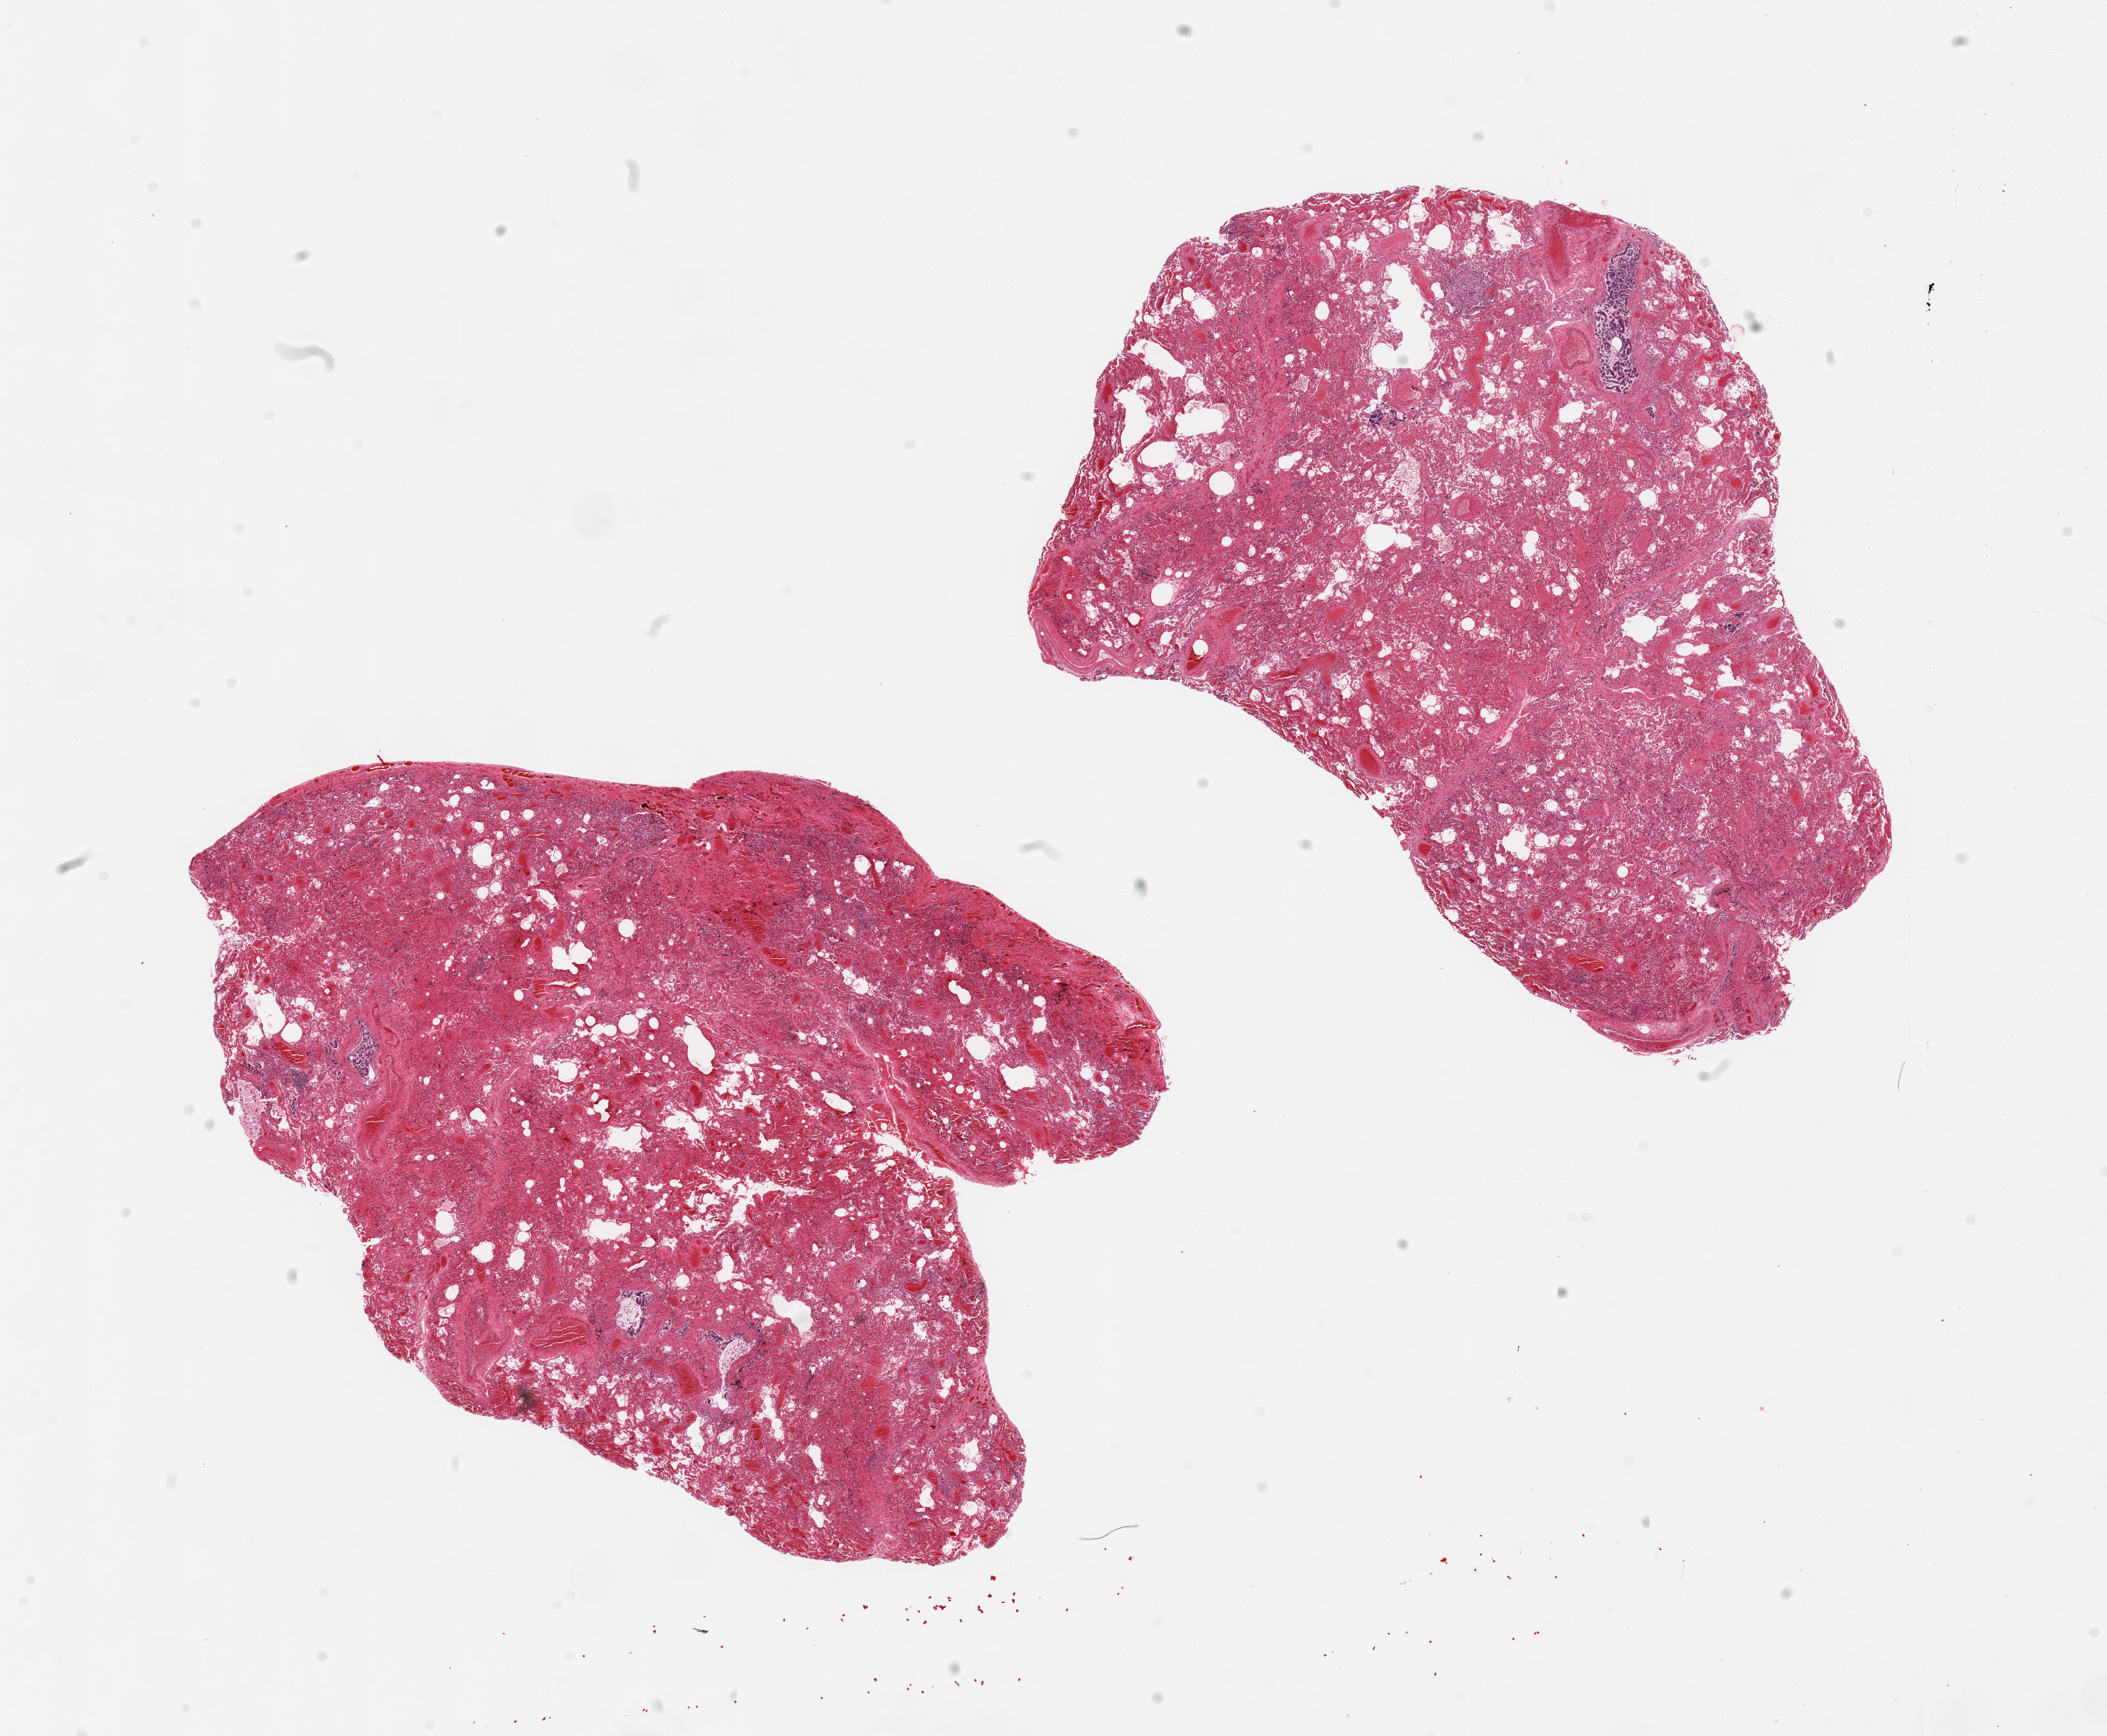
Whole-slide image, hematoxylin and eosin (H&E) stain — low-resolution overview of the scanned area, about 22.6 x 18.7 mm (from a 20x scan), PAXgene-fixed paraffin-embedded (PFPE) section, sampled site (target tissue): lung, tissue donor sample. Donor: male.
• pathologist's review note for this sample: 2 pieces, marded congestion